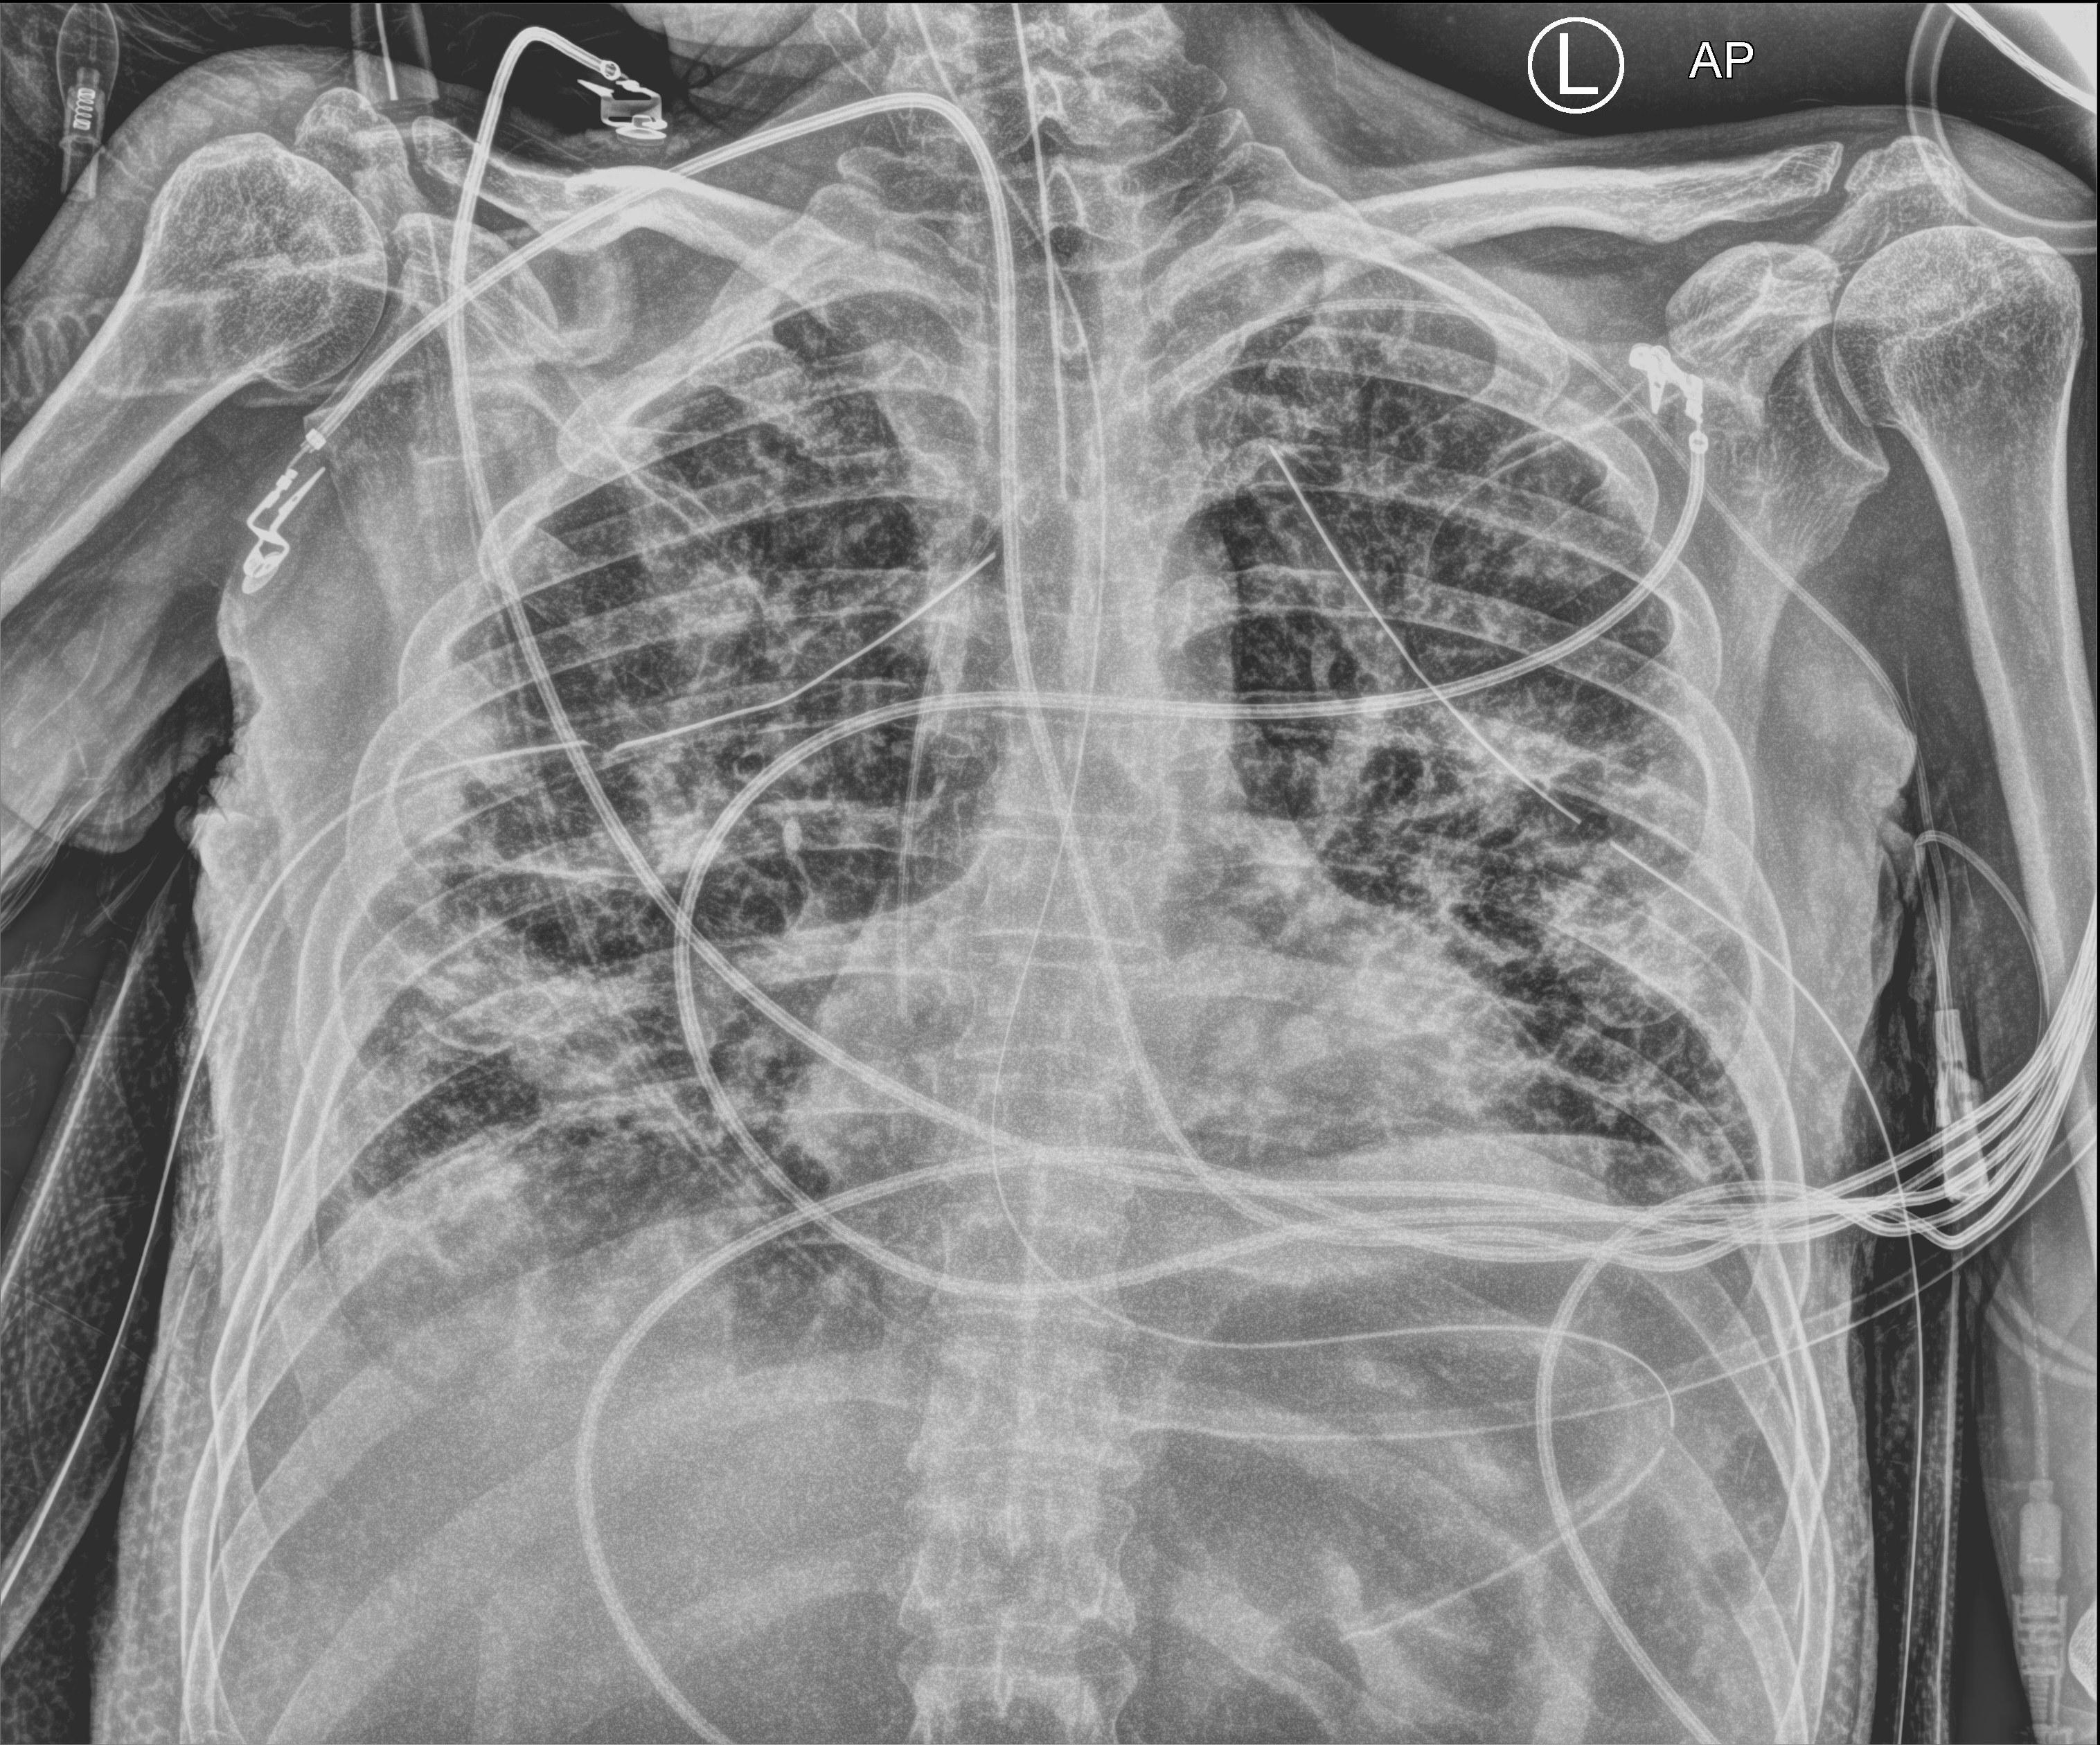
Portable chest radiograph; anteroposterior (AP) projection. Male patient hospitalised with COVID-19, age 18–59 years.
From the hospital-stay record, not from the radiograph (when in the stay this image was taken is not recorded): mechanically ventilated during this hospital stay: yes; chronic kidney disease (admission record): no; admitted to intensive care during this hospital stay: yes.